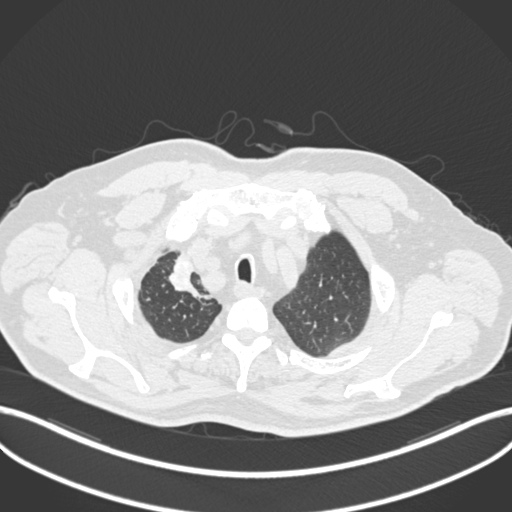
Chest CT, one axial slice. Slice 177 of 255 in the series (ordered by position). Lung window (W 1500 / L -600 HU). 1 mm slice thickness. 512 × 512 image matrix, field of view 400 × 400 mm. Male patient, age 60 years. Case-level facts recorded for this patient, not image findings: clinical TNM (as recorded): T1b N1 M0.
Annotated regions visible in this slice (rectangle marked by the reading radiologist):
- lung tumour (recorded histology: squamous cell carcinoma): bounding box (x1, y1, x2, y2) in pixels: (164, 251, 208, 303)